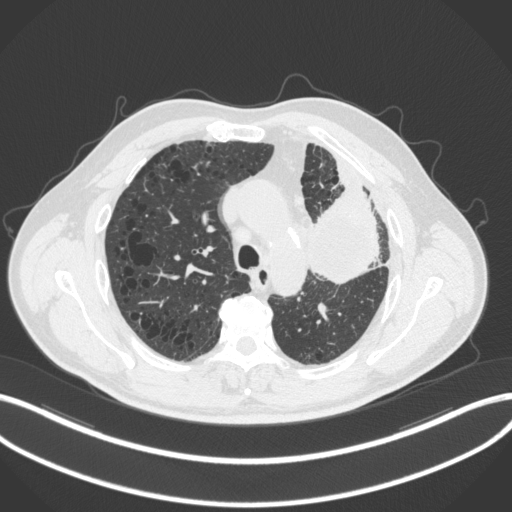
Chest CT, one axial slice; position 209 of 286 along the scan axis; 120 kVp; lung window (W 1500 / L -600 HU); 1 mm slice thickness; 512 × 512 image matrix, field of view 400 × 400 mm. Male patient, age 68 years. Case-level facts recorded for this patient, not image findings: clinical TNM (as recorded): T3 N3 M1.
Annotated regions visible in this slice (bounding box drawn by a radiologist):
- lung tumour (recorded histology: adenocarcinoma): box from (x=306, y=174) to (x=379, y=289) px